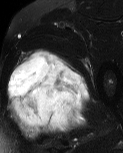
MRI of an extremity soft-tissue mass, one axial slice. Slice 37 of 60 in the series (ordered by position). T2-weighted fat-saturated. MR volume resampled by the dataset authors to the PET/CT grid (not the native acquisition matrix). 3.27 mm slice thickness. 123 × 153 image matrix, field of view 120 × 149 mm. Male patient. From the clinical record (not read from this slice): histological type: pleiomorphic liposarcoma; grade: high; site of the primary tumour: left thigh.
Structures marked on this image (expert contour drawn on MRI and transferred to this co-registered scan by the dataset authors):
- gross tumour volume including surrounding oedema: bounding box [x1, y1, x2, y2] px = [8, 49, 89, 140]
- gross tumour volume (mass): [8, 52, 89, 128]